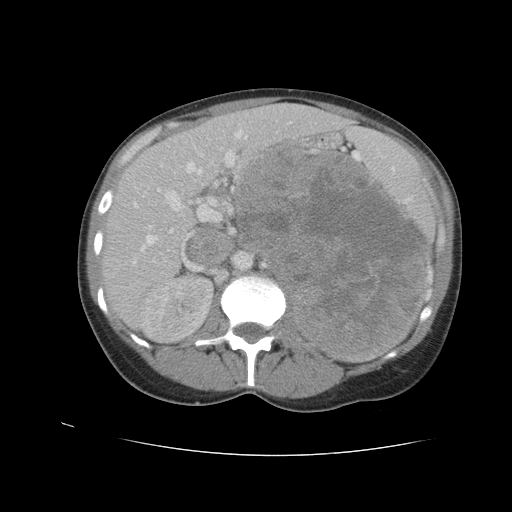
Contrast-enhanced abdominal CT, one axial slice. Slice 63 of 90 in the series (ordered by position). Reconstruction kernel STANDARD. Intravenous contrast given. Soft-tissue window (W 400 / L 40 HU). 5 mm slice thickness. 512 × 512 image matrix, field of view 360 × 360 mm. Female patient. From the clinical record (not read from this slice): diagnosis: adrenocortical carcinoma; tumour side: left adrenal; tumour size at pathology: 18 cm; Ki-67 index: 11 %; stage (as recorded): 3.
Outlined on this slice (semi-automatic segmentation, software-assisted and operator-edited):
- mass: bounding box (x1, y1, x2, y2) in pixels: (244, 149, 428, 354)